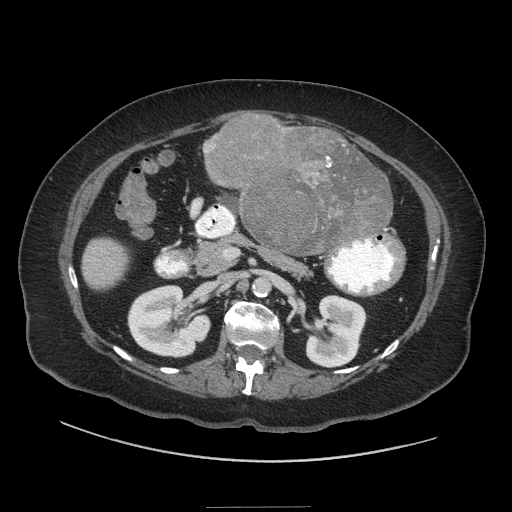
Contrast-enhanced abdominal CT (liver protocol), one axial slice; slice 7 of 81 in the series (ordered by position); soft-tissue window (W 400 / L 40 HU); 512 × 512 image matrix. Case-level facts recorded for this patient, not image findings: diagnosis: hepatocellular carcinoma (patient treated with transarterial chemoembolisation; whether this scan precedes or follows treatment is not stated here); TNM stage (as recorded): Stage-II; Child-Pugh class: A; tumour differentiation: moderately differentiated.
Structures marked on this image (semi-automatically segmented with operator editing):
- liver parenchyma outside the tumour (the mass and vessels are separate outlines, so this box may not span the whole liver): bounding box (x1, y1, x2, y2) in pixels: (82, 124, 392, 290)
- mass: (205, 116, 391, 254)